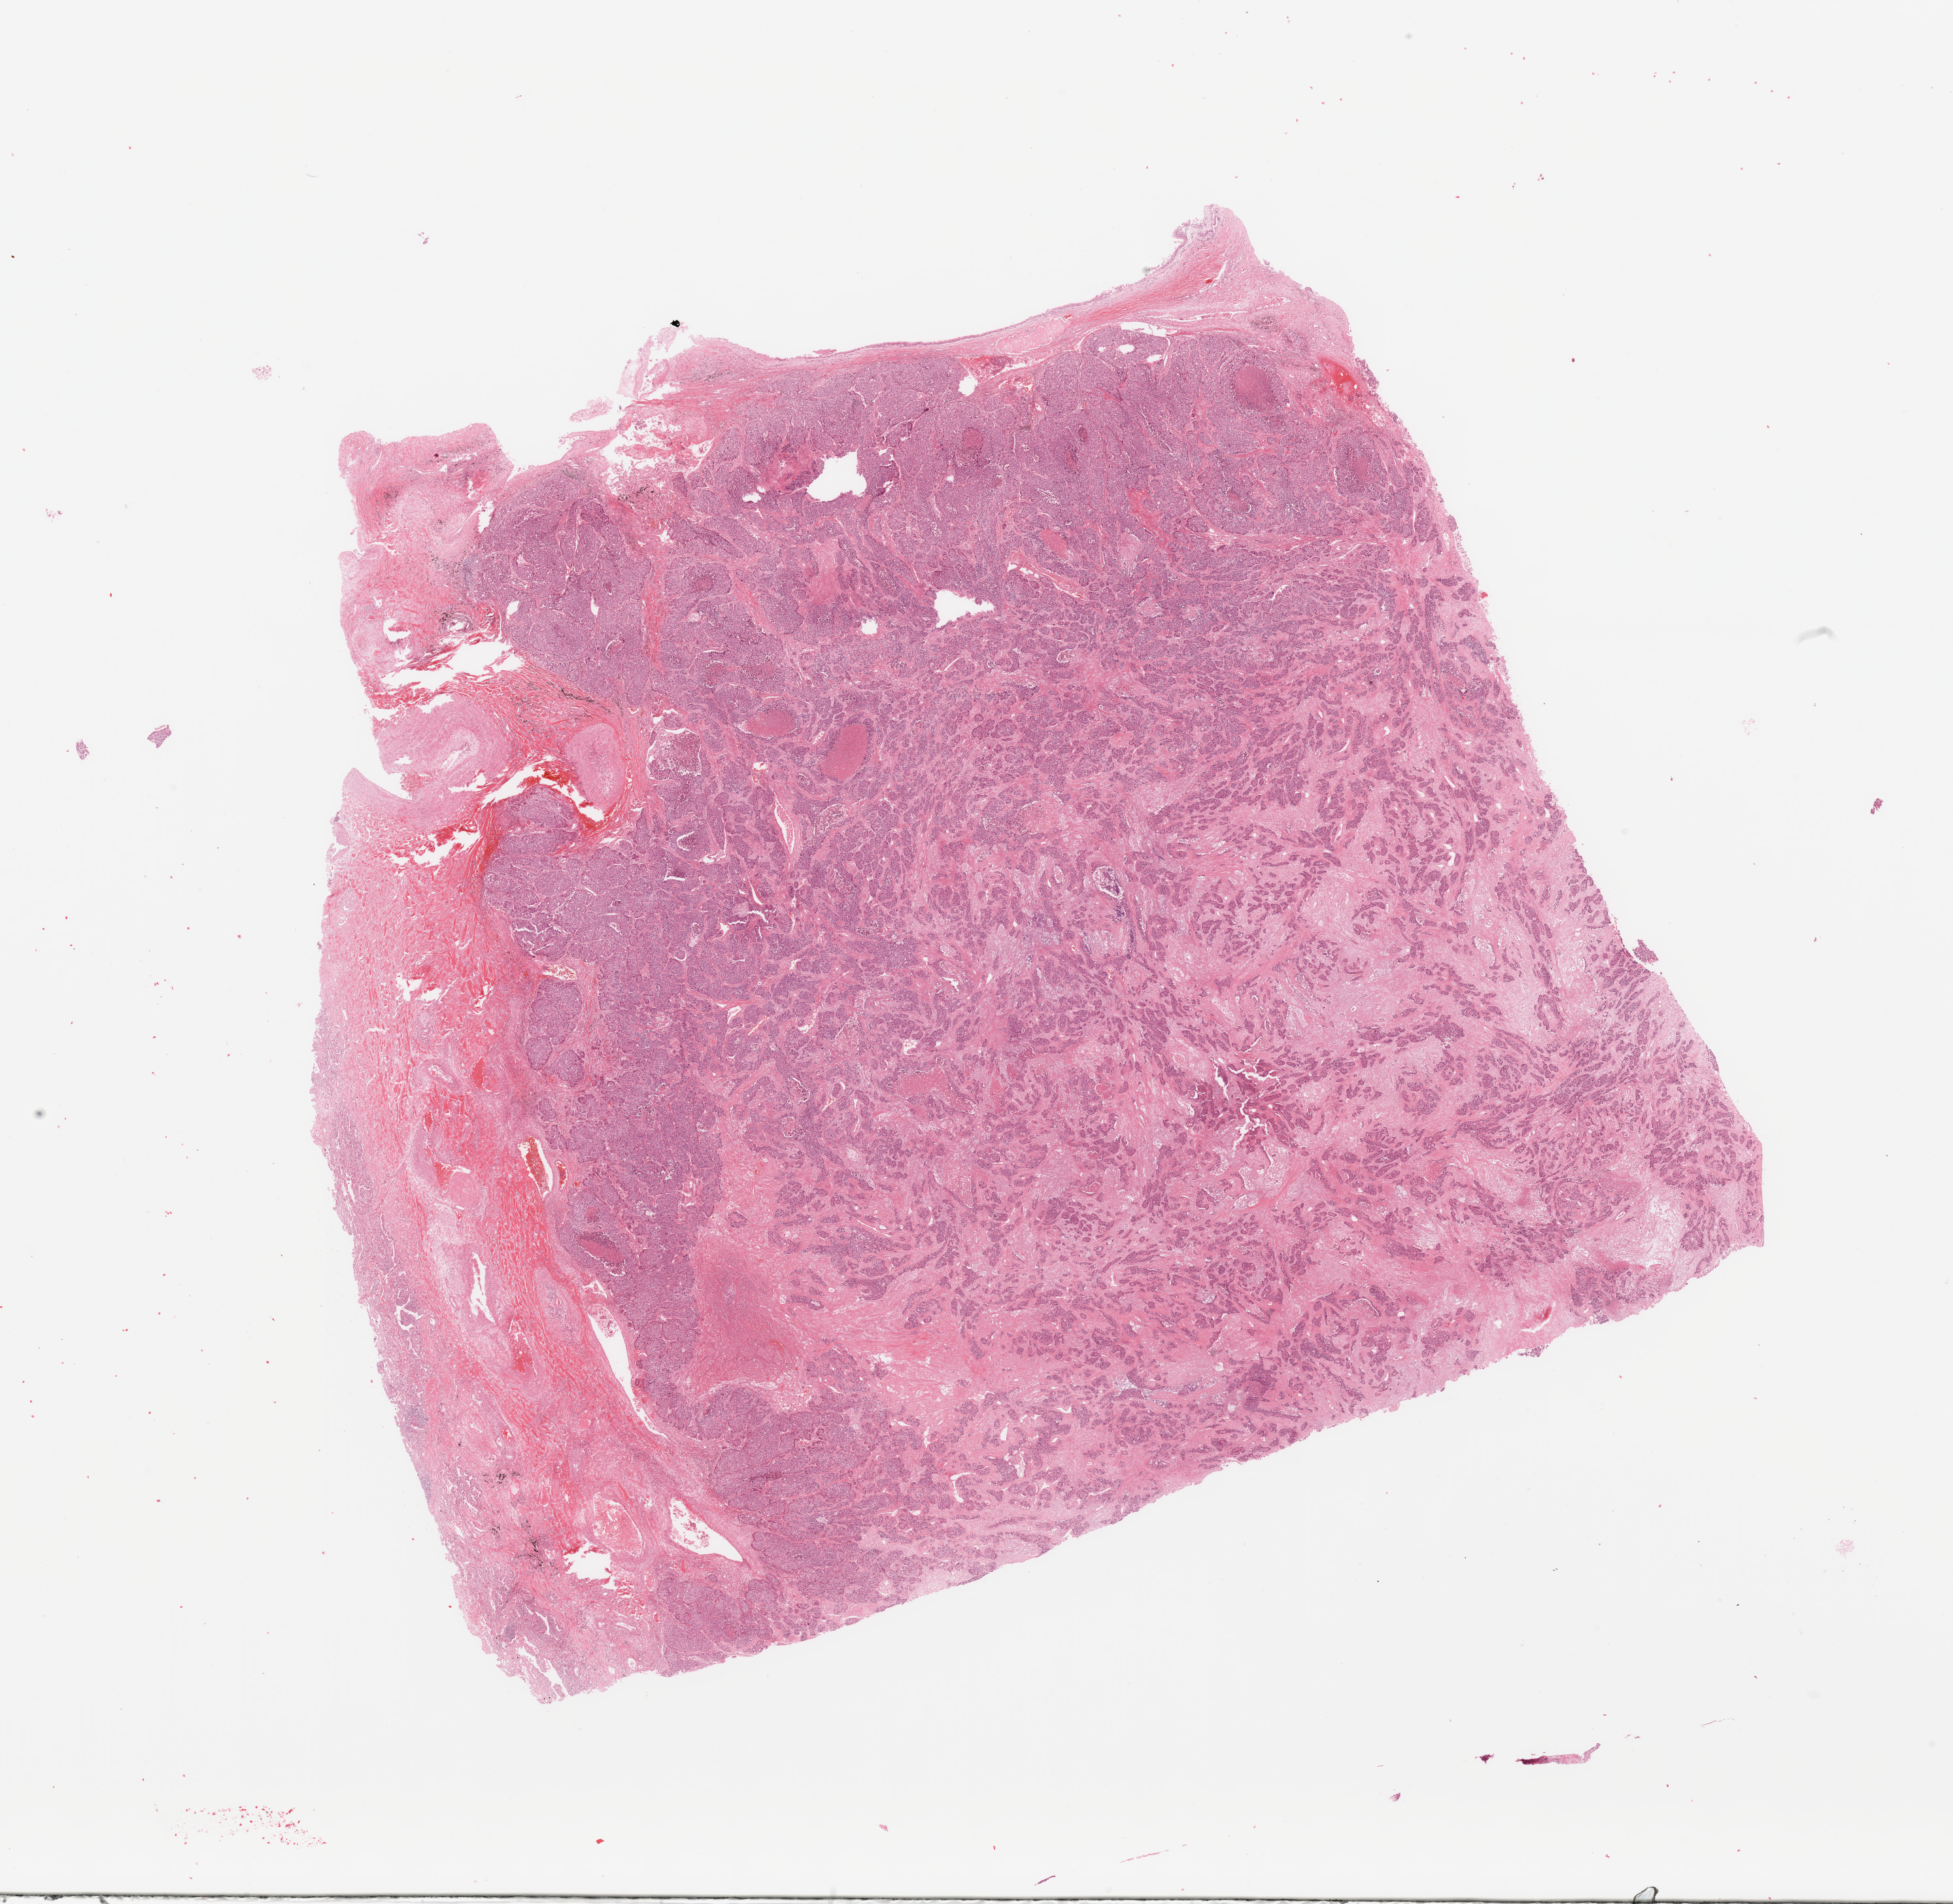
Whole-slide histology image, H&E — whole scanned area (about 23.6 x 23.0 mm) shown as a low-resolution overview; tumour tissue sample, sampled site: lung. 58-year-old male patient. Histologic grade: G3 (poorly differentiated). Slide review estimates, as recorded: tumour nuclei 75%, necrosis 15%.
* diagnosis: Adenocarcinoma, NOS
* AJCC pathologic stage: IB